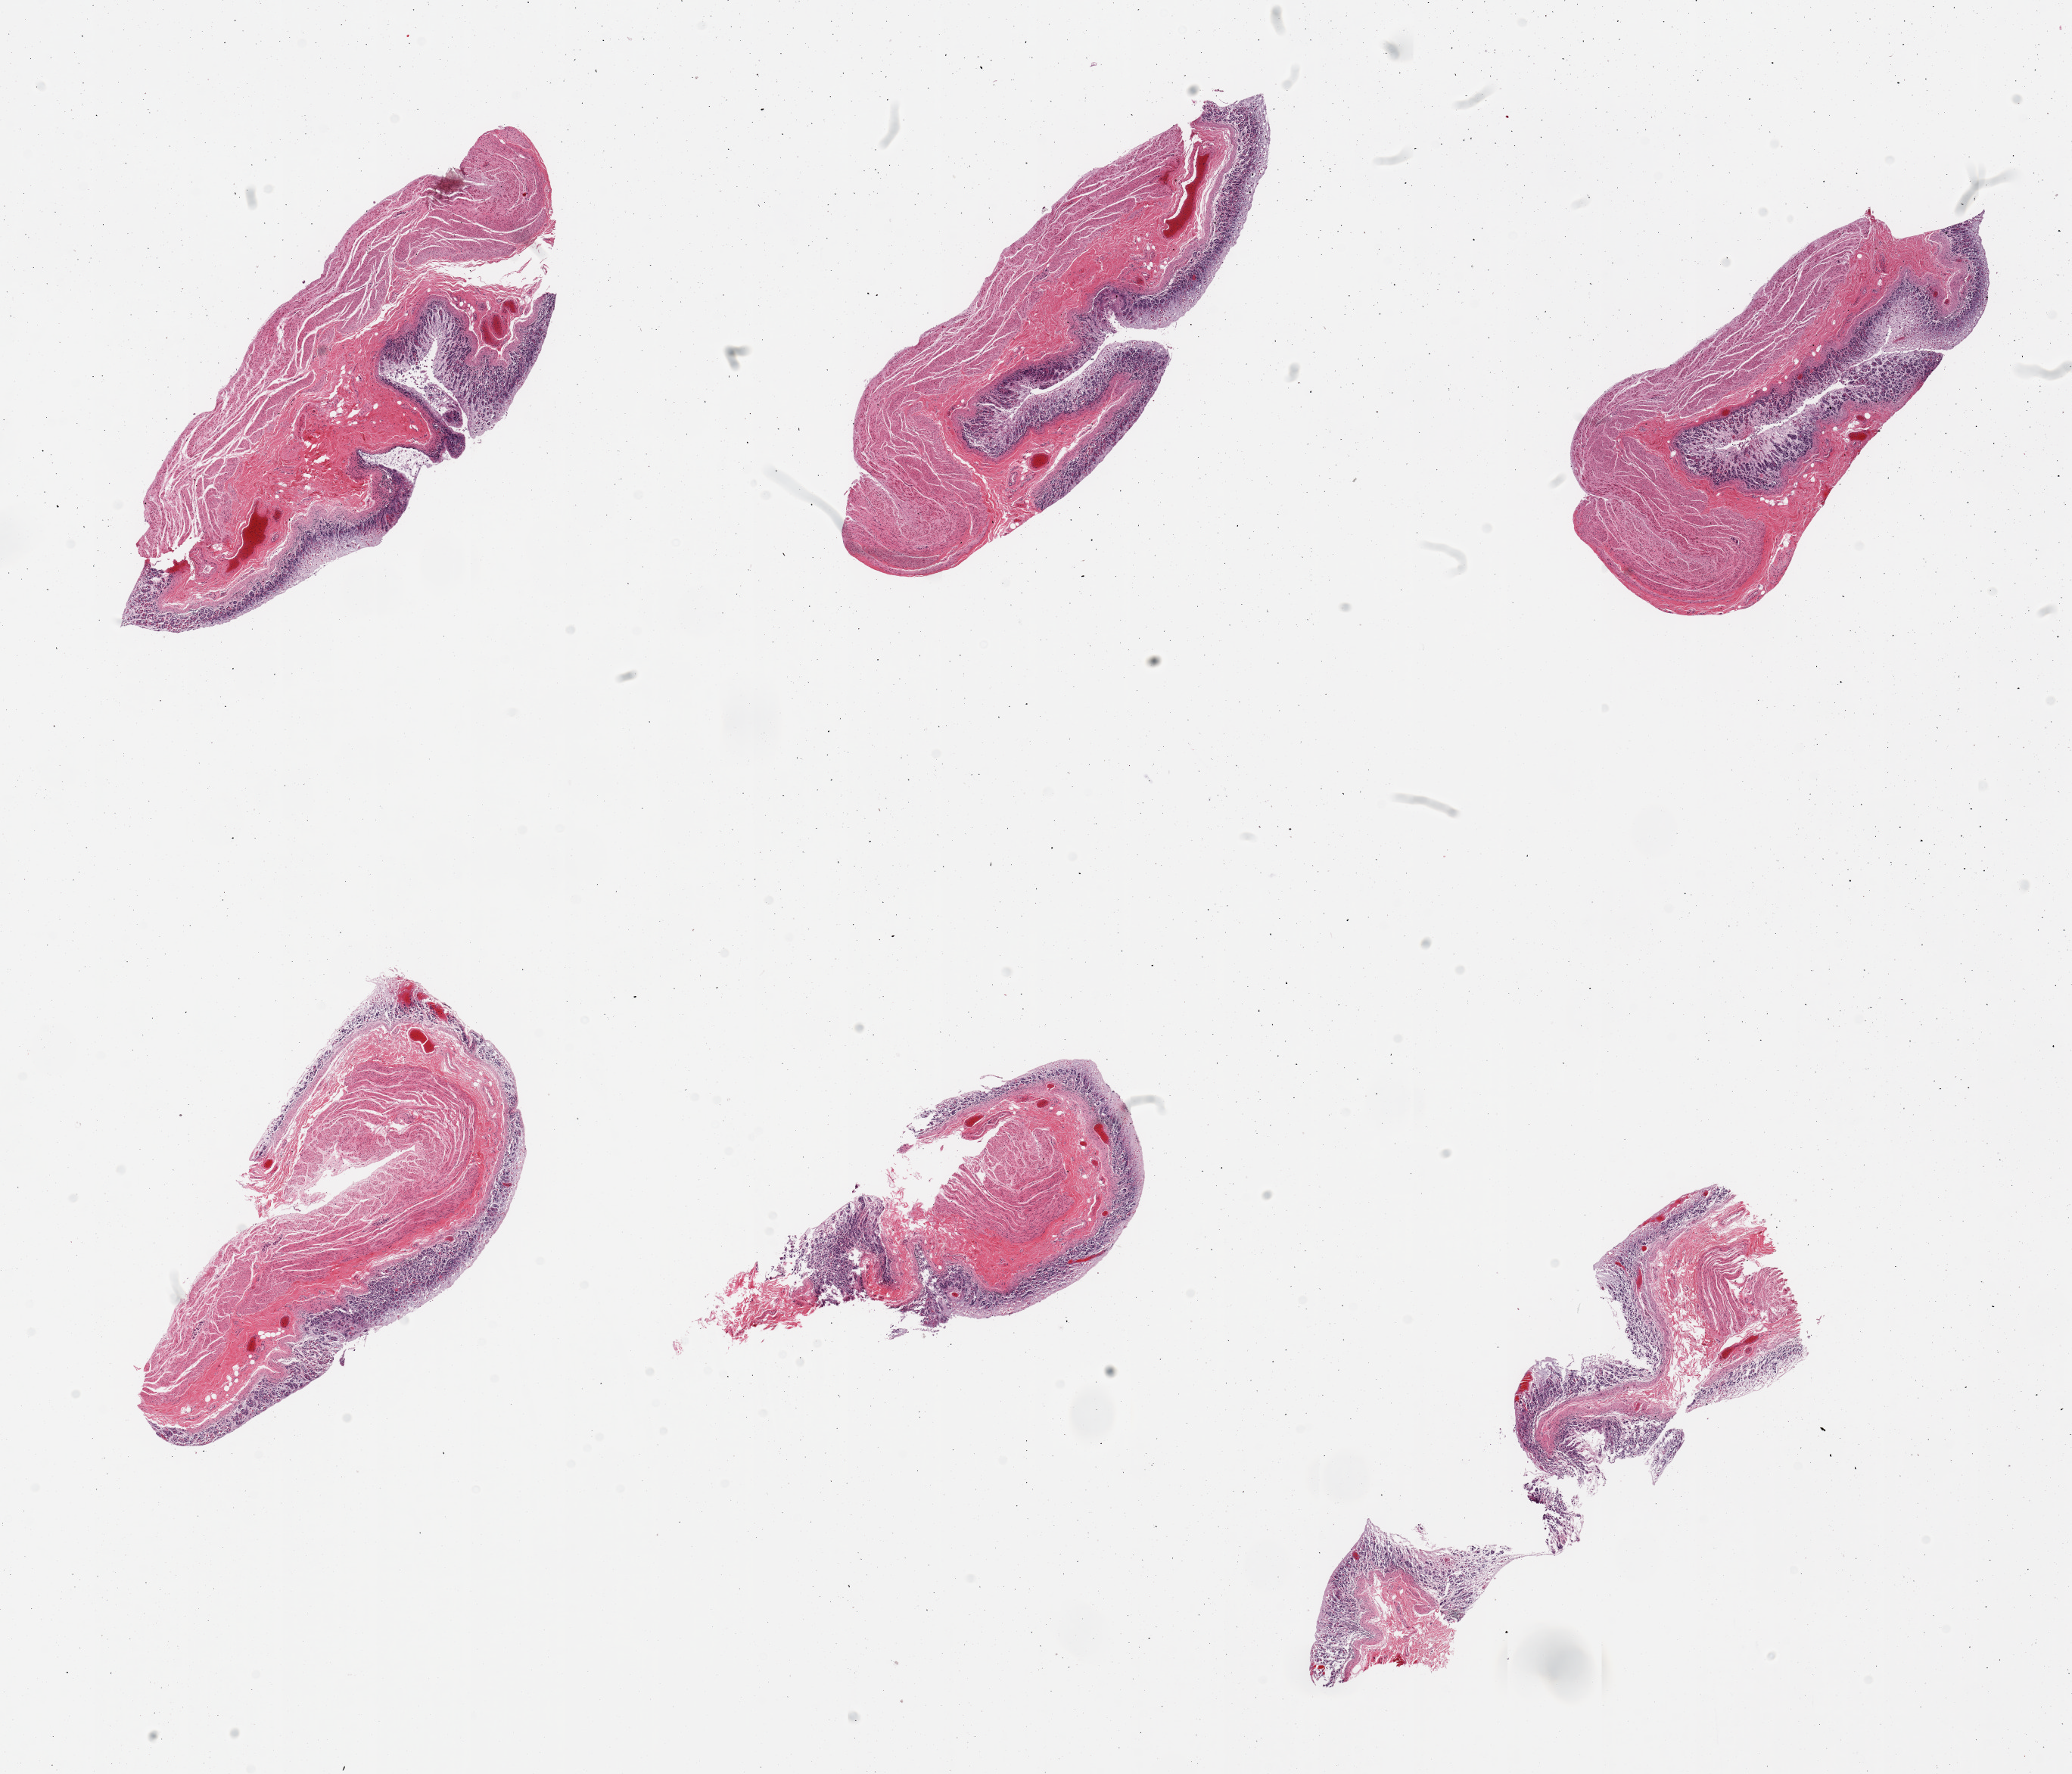
H&E whole-slide image — low-resolution overview of the scanned area, about 21.7 x 18.5 mm, PAXgene-fixed paraffin-embedded (PFPE) section, sampled site (target tissue): stomach, donor tissue sample. Donor: female.
- pathologist's review note for this sample: 6 pieces; epithelium autolyzed; muscle intact